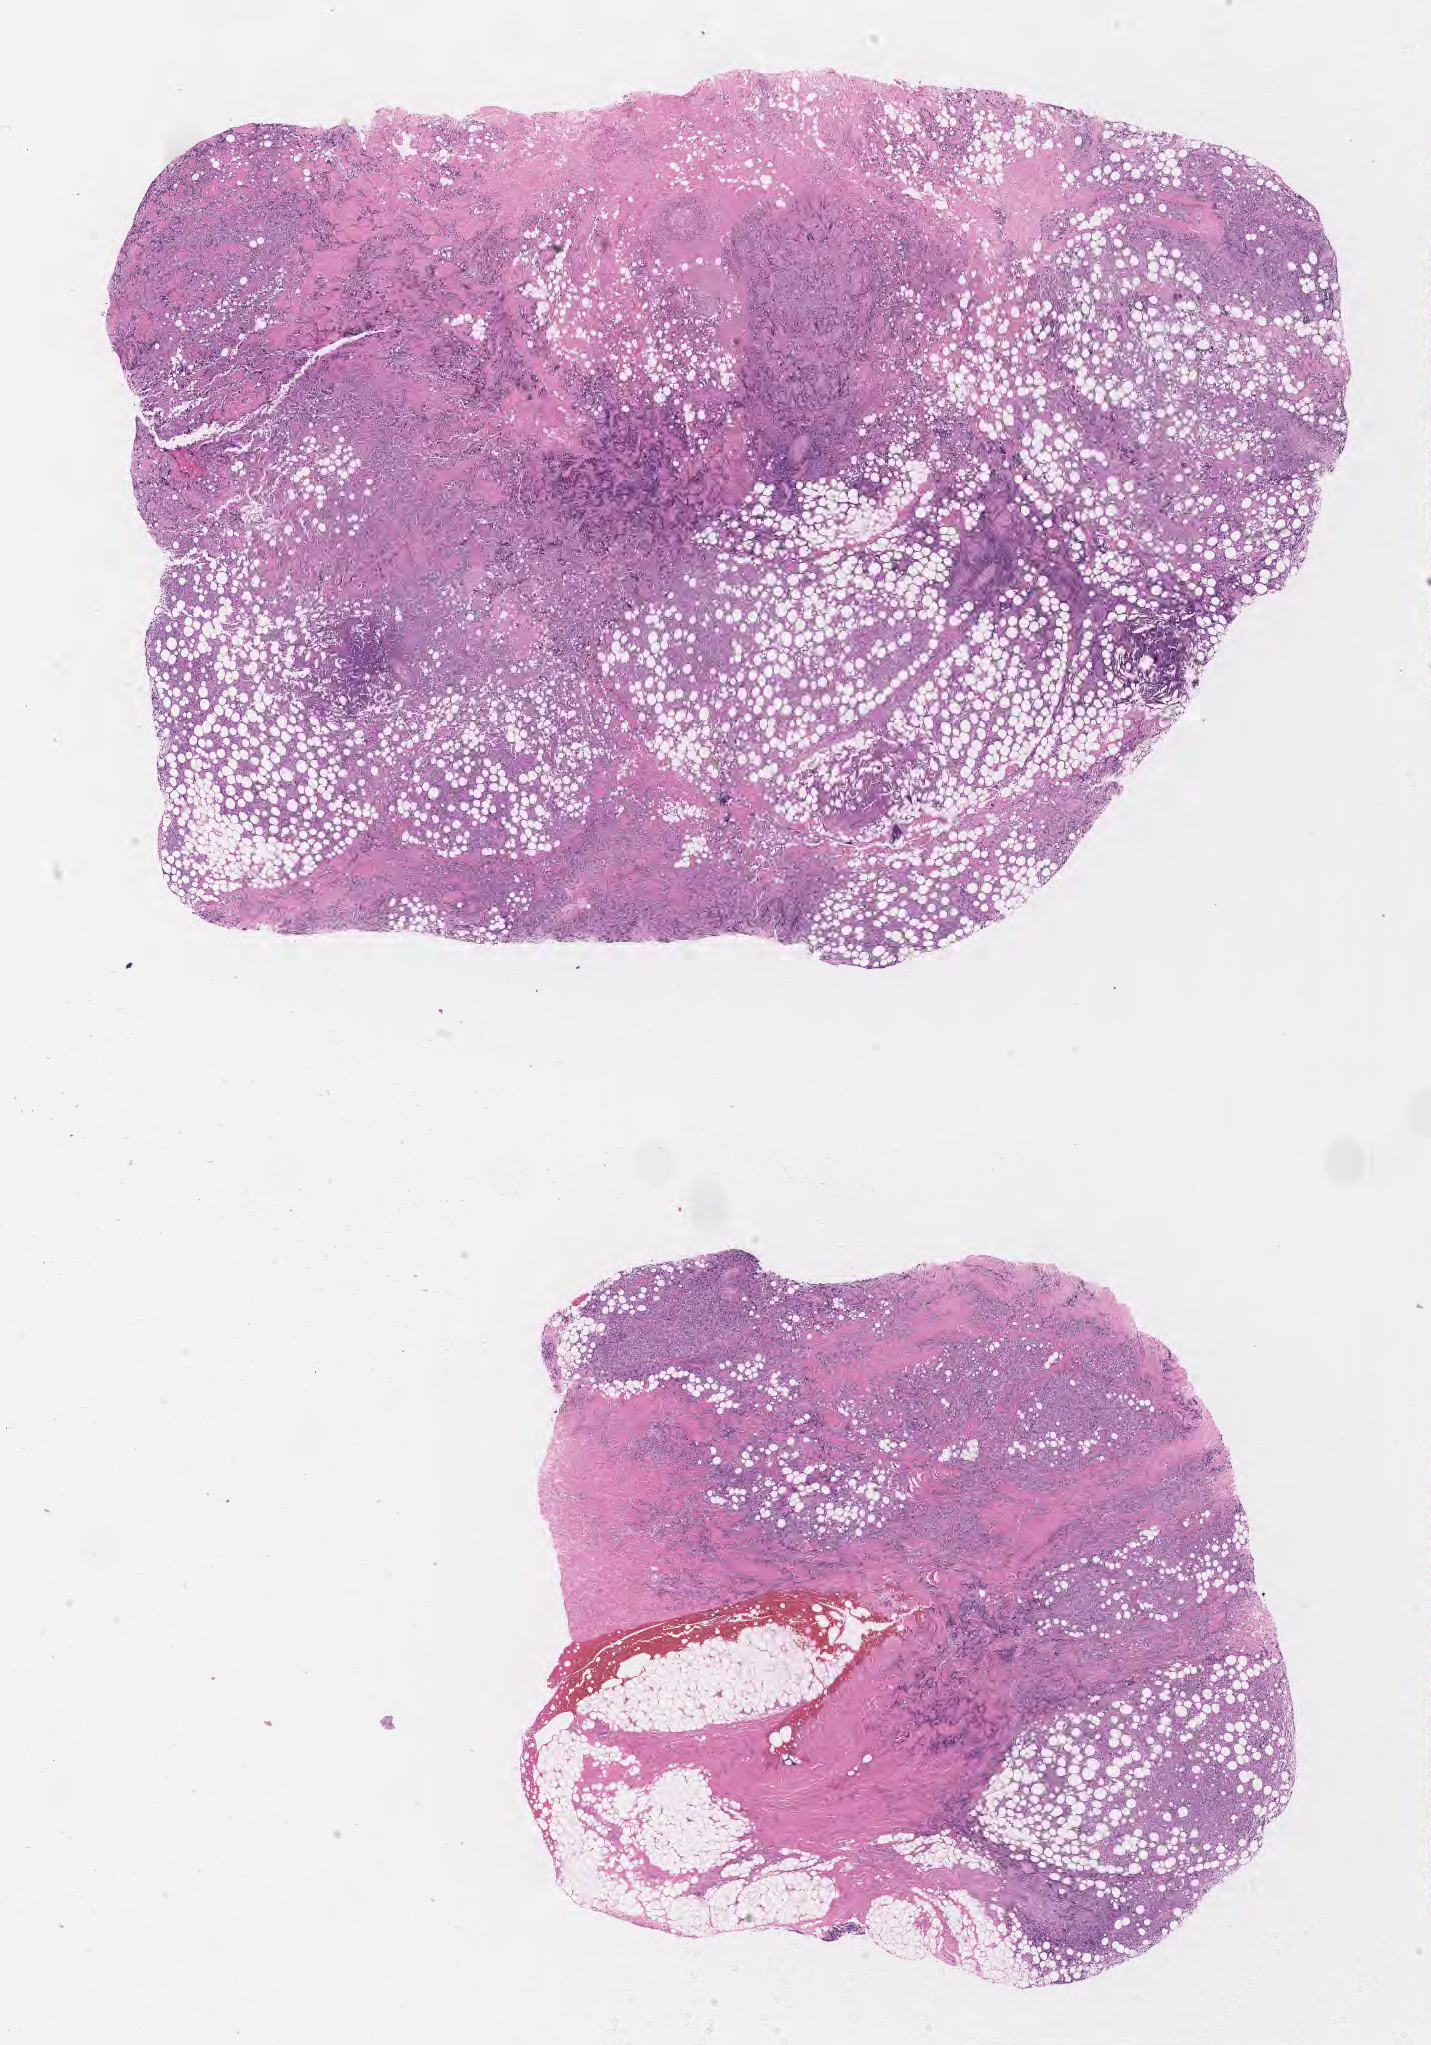
Digitized haematoxylin and eosin-stained section, a low-resolution overview of the entire scanned area, about 11.6 x 16.5 mm; specimen: tumor tissue; anatomic site: kidney. Patient male; 63 years old.
Histologic diagnosis: Diffuse large B-cell lymphoma, NOS.